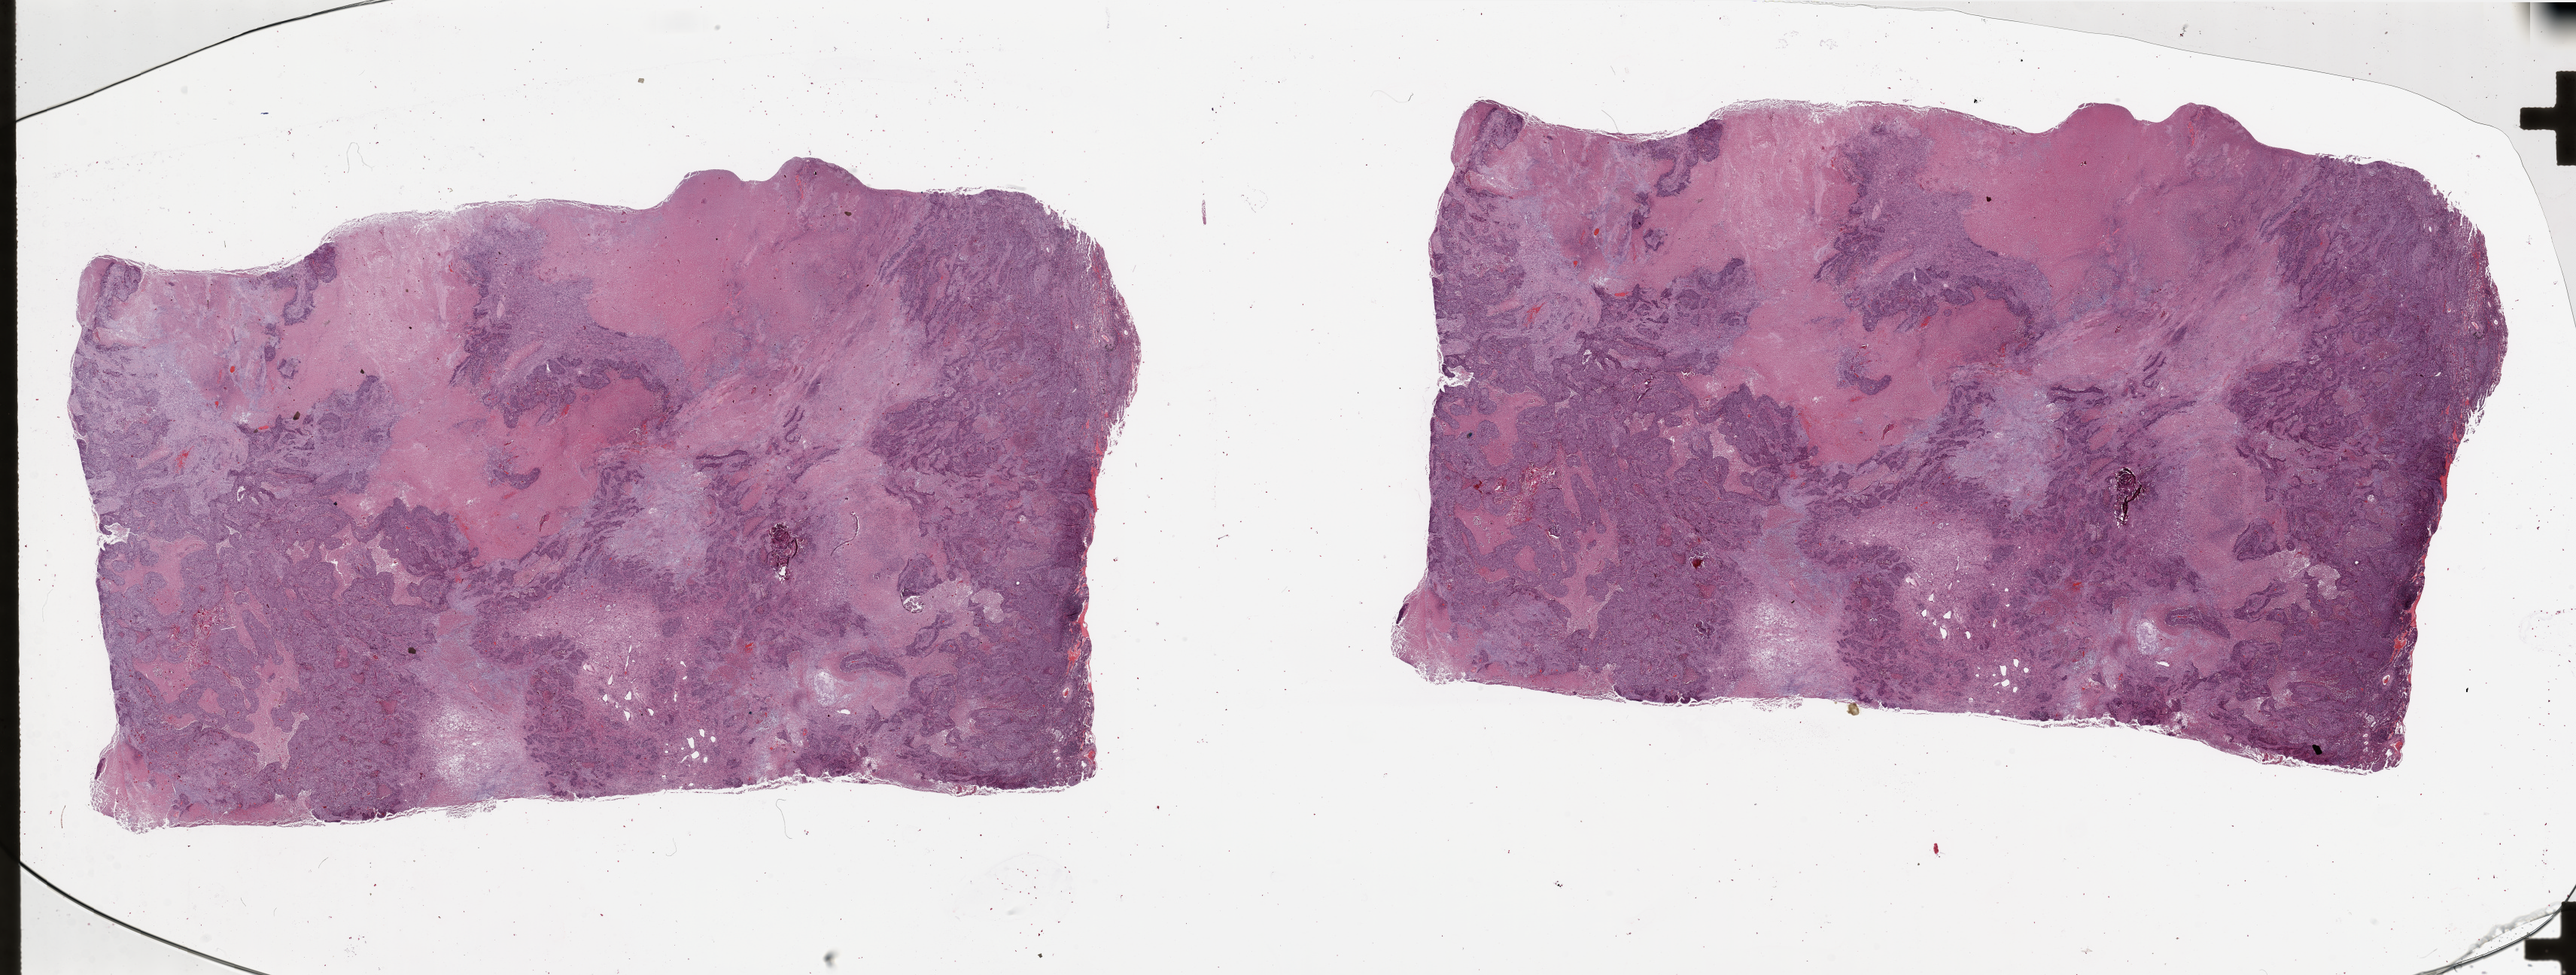
Digitized H&E-stained tissue section (whole slide) — shown as a low-resolution overview of the whole scanned area (about 54.1 x 20.5 mm); lung, tumour tissue. Male, 74 y/o. Histologic grade: G2 (moderately differentiated).
Diagnosis: Squamous cell carcinoma, NOS. Primary tumour site (as recorded): right middle lobe. AJCC pathologic stage: IIA.